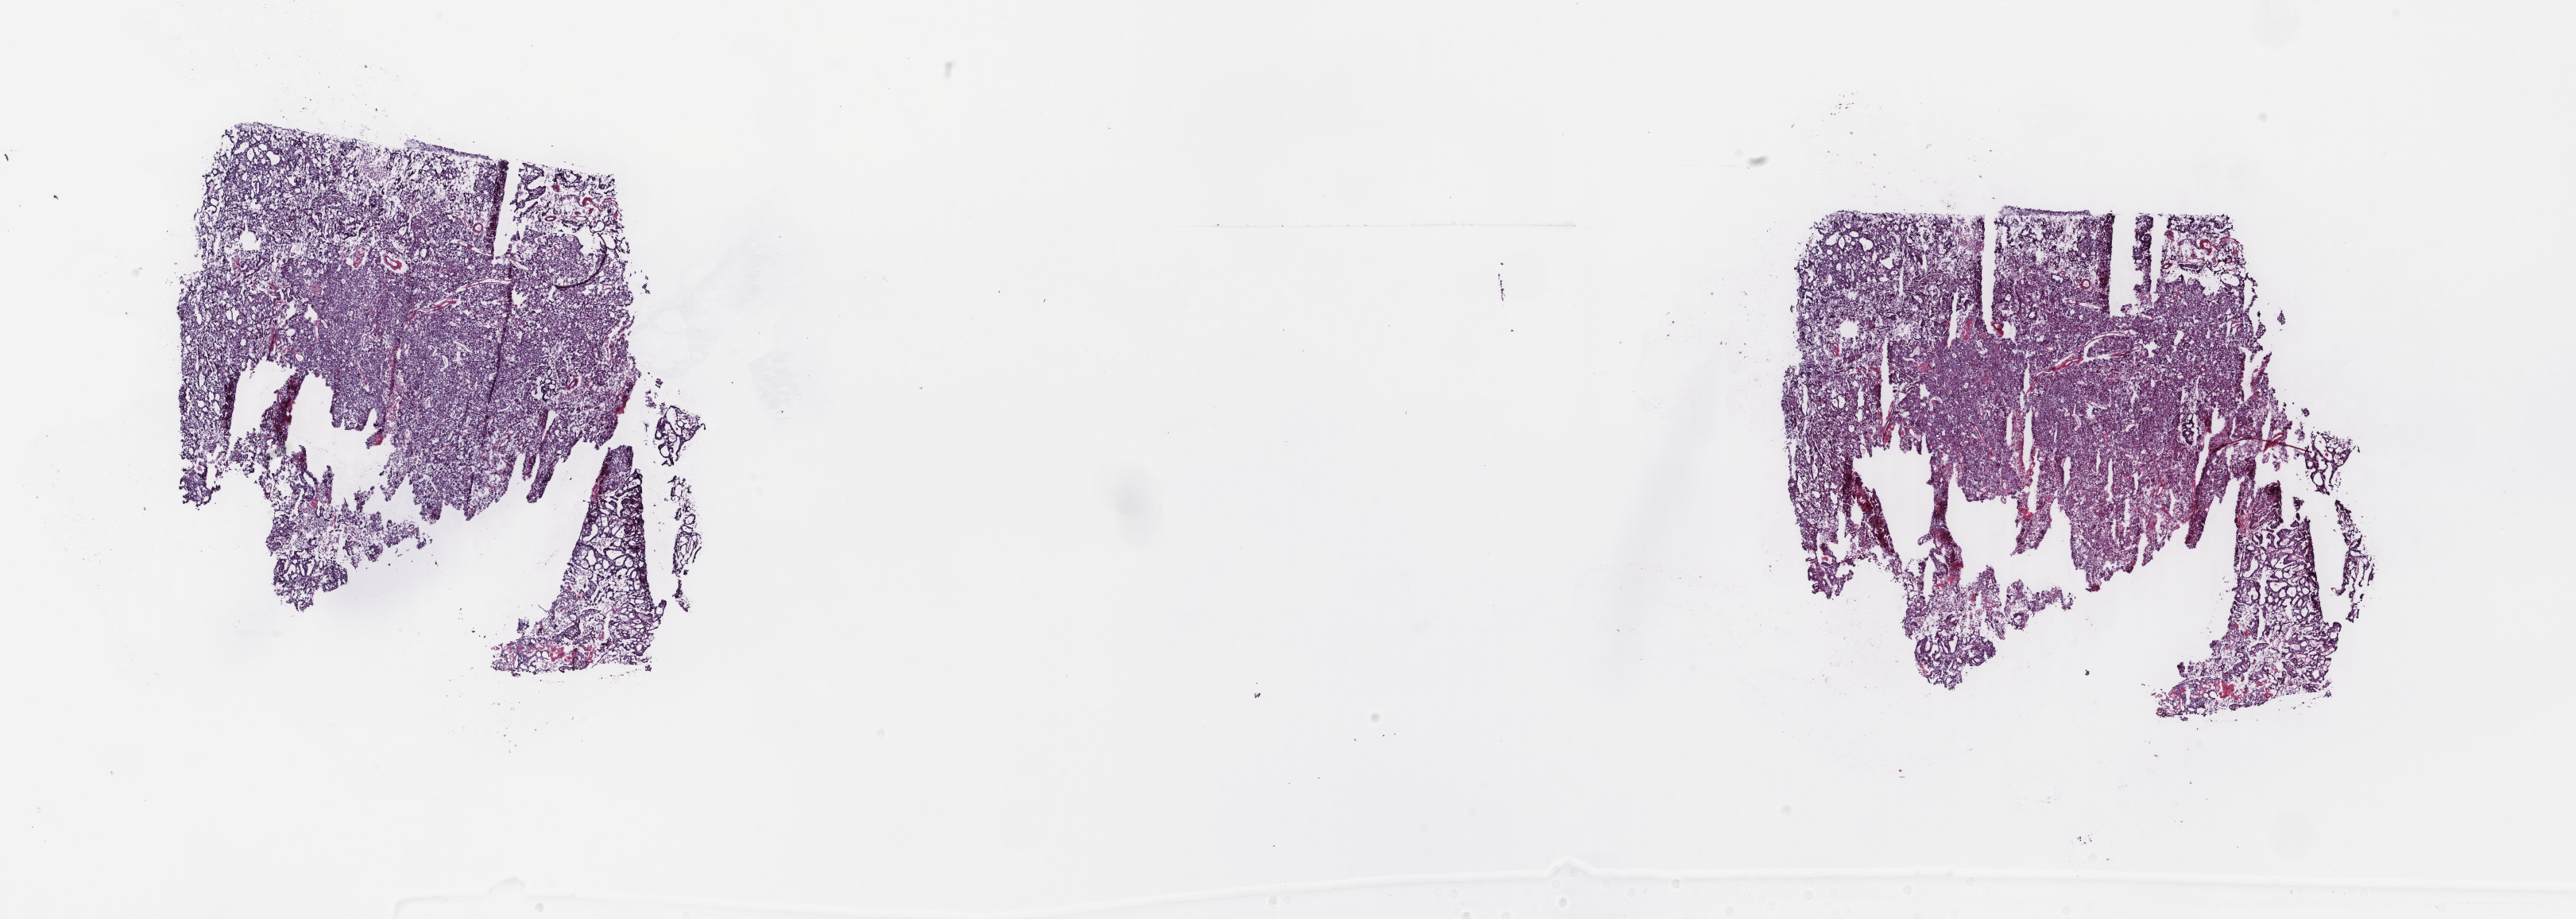
Hematoxylin and eosin (H&E) stained whole-slide image — whole scanned area (about 25.7 x 9.2 mm, from a 40x scan) shown as a low-resolution overview, frozen section, sample: primary tumour, uterus. Female, age 73 years at initial diagnosis. Histologic grade: G3 (poorly differentiated). Pathologist review of this section (percent, as recorded): tumour cells 80%, tumour nuclei 80%, normal cells 0%, stromal cells 10%, necrosis 10%. Infiltration values recorded for this section: lymphocyte infiltration 30%, monocyte infiltration 20%, neutrophil infiltration 30%.
FIGO stage: IVB. Pathologic diagnosis: Endometrioid adenocarcinoma, NOS (endometrium).